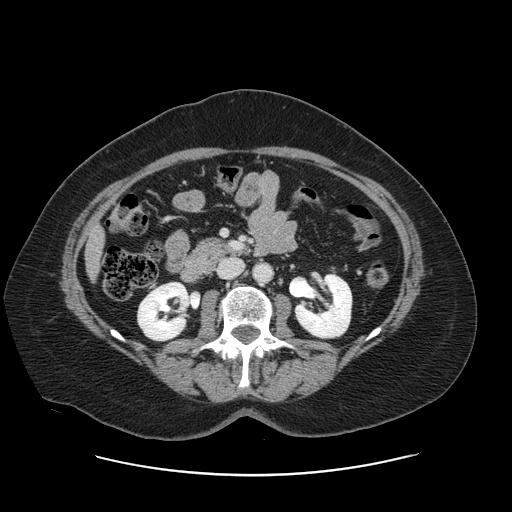
Contrast-enhanced abdominal CT, one axial slice. Slice 44 of 161 in the series (ordered by position). 120 kVp. Soft-tissue window (W 400 / L 40 HU). 2.5 mm slice thickness. 512 × 512 image matrix, field of view 398 × 398 mm. Female patient, age 62 years. Case-level facts recorded for this patient, not image findings: diagnosis: colorectal cancer liver metastases, imaged before liver resection; multiple liver metastases: no; largest metastasis: 2.5 cm; disease in both lobes: no.
Structures marked on this image (manually delineated by an expert):
- liver: bounding box <88,232,103,274> (left, top, right, bottom; pixels)